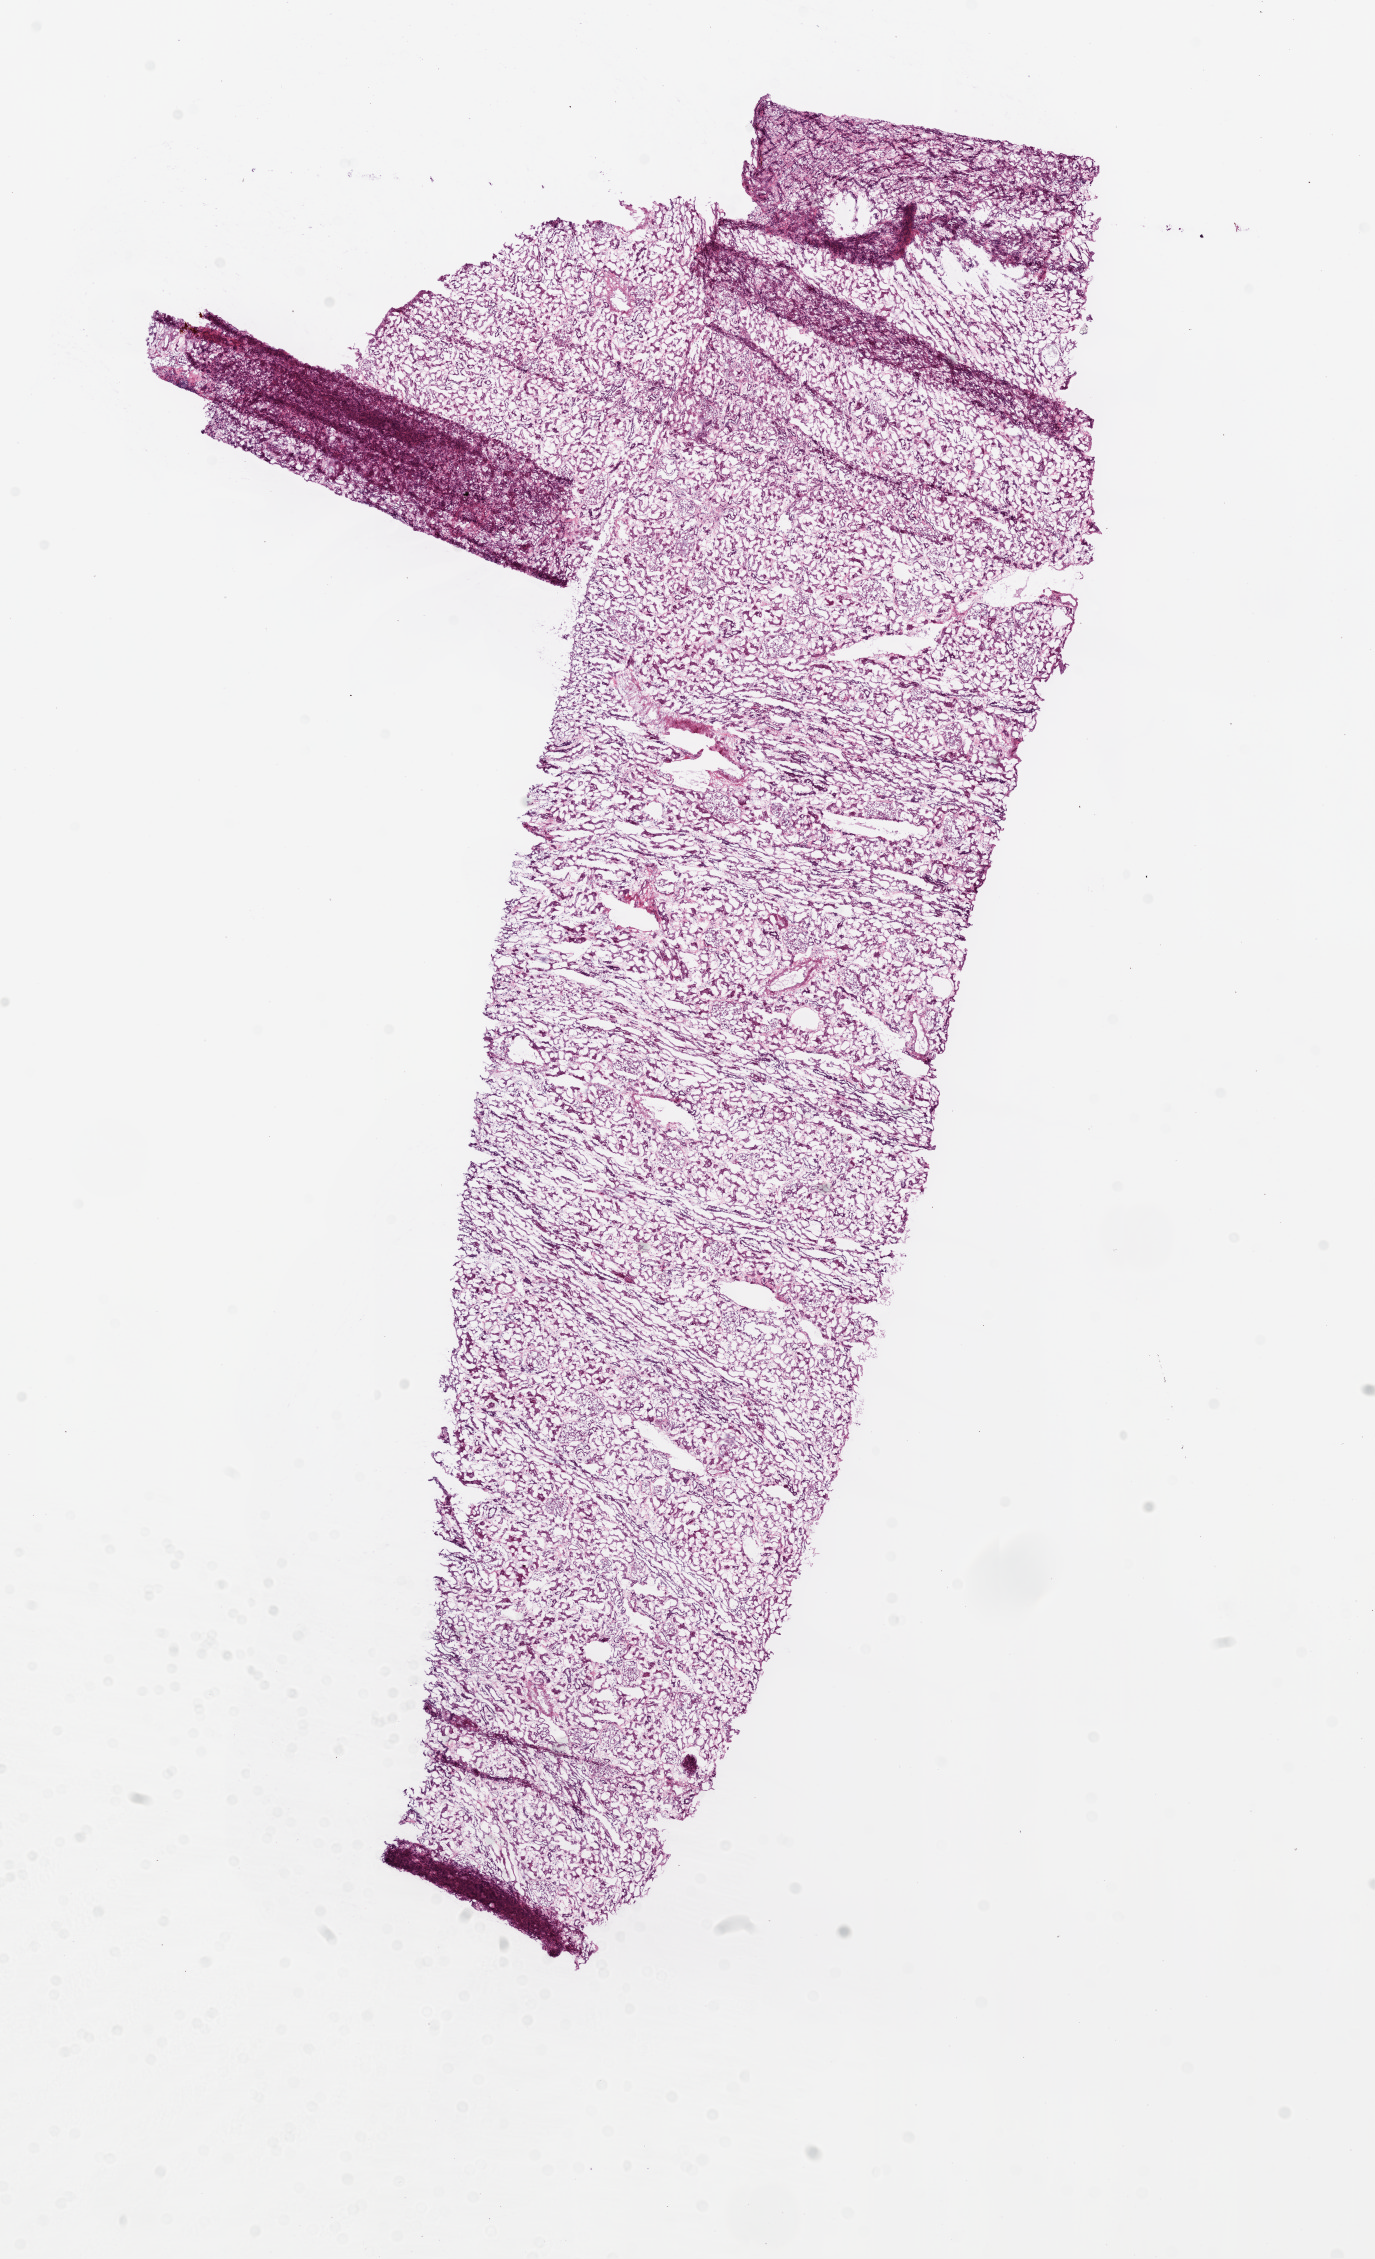
Digitized Hematoxylin and eosin (H&E) stained tissue section (whole slide) — a low-resolution overview of the entire scanned area, about 11.0 x 18.1 mm. Frozen section. Kidney, solid tissue normal (non-tumour tissue) sample. Patient: male, age at initial diagnosis 42 years.
This section: solid tissue normal (non-tumour) sample from the same patient. Patient diagnosis: Clear cell adenocarcinoma, NOS.